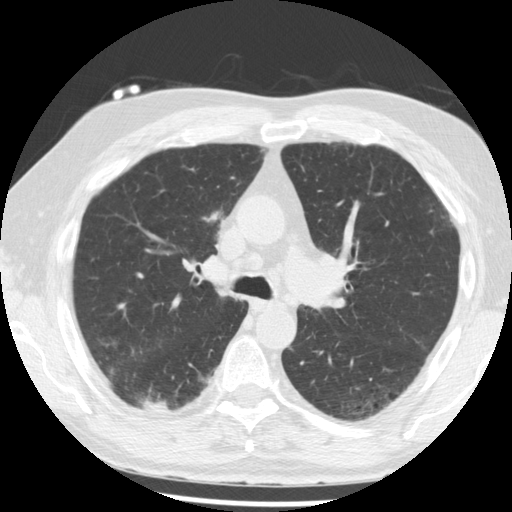
Low-dose screening chest CT, one axial slice; slice 137 of 221 in the series (ordered by position); lung window (W 1500 / L -600 HU); 512 × 512 image matrix, field of view 350 × 350 mm.
Outlined on this slice (outlined manually by an expert reader):
- lesion 1 (tumor, lower lobe of right lung): bounding box <143,400,172,413> (left, top, right, bottom; pixels)